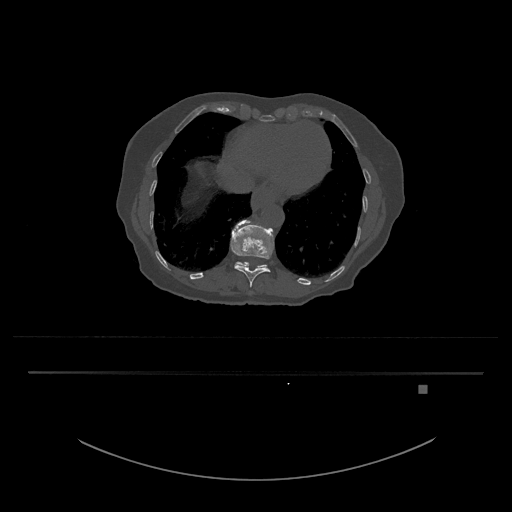
CT including the spine, one axial slice. Position 654 of 797 along the scan axis. Reconstruction kernel Br40s/3. Bone window (W 1800 / L 400 HU). 0.5 mm slice thickness. 512 × 512 image matrix. Female patient, age 57 years. Case-level facts recorded for this patient, not image findings: primary cancer: cervical.
Annotated regions visible in this slice (semi-automatic segmentation, software-assisted and operator-edited):
- T11 vertebra: bounding box [x1, y1, x2, y2] px = [230, 219, 274, 288]
- T12 vertebra: [235, 261, 267, 268]